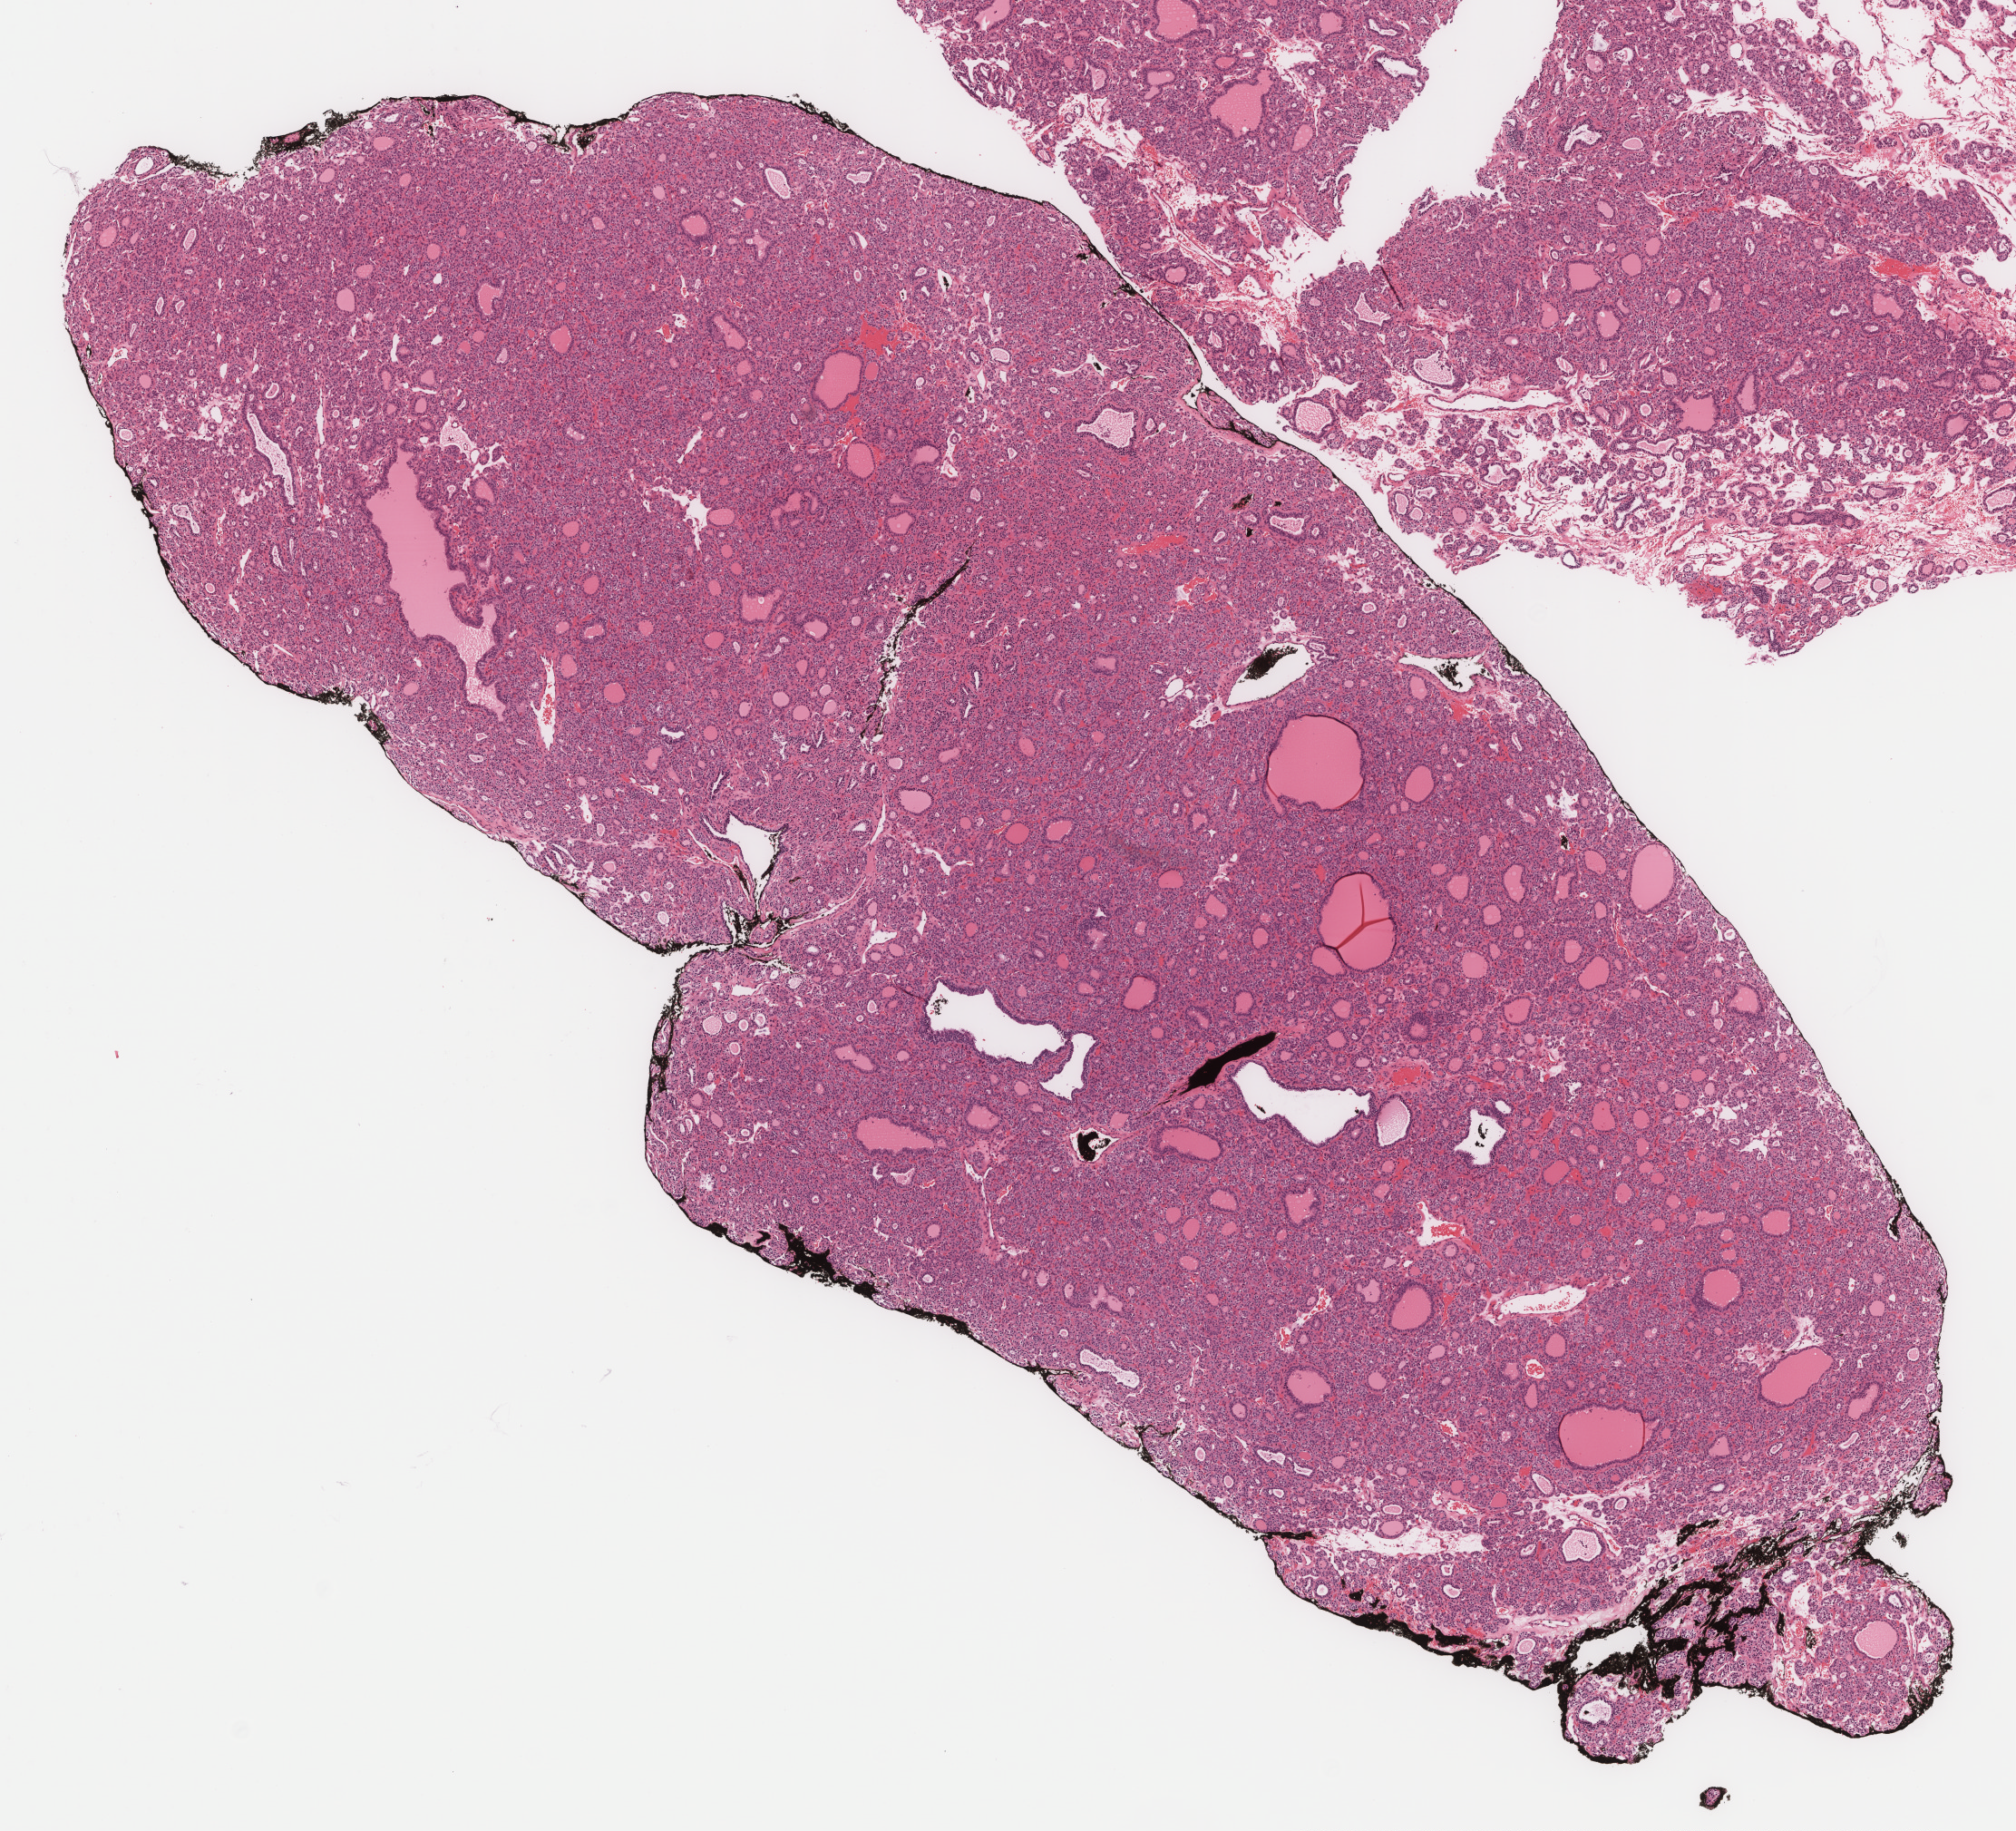
Whole-slide histology image, Hematoxylin and eosin (H&E) stained, shown as a low-resolution overview of the whole scanned area (about 9.0 x 8.1 mm); FFPE section; thyroid, primary tumour sample. Female, age 42 years at initial diagnosis.
AJCC pathologic stage: I. Laterality: left. Diagnosis: Papillary carcinoma, follicular variant (thyroid gland).